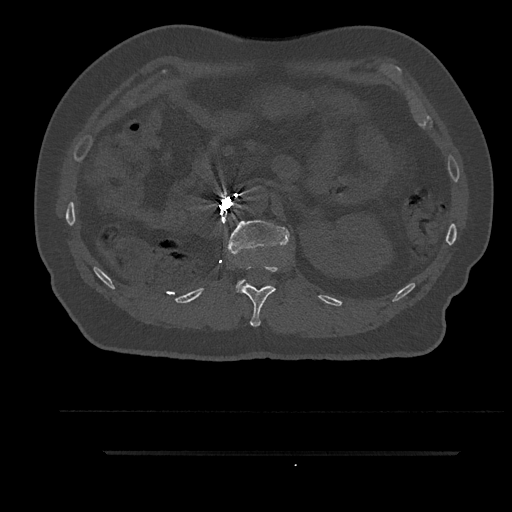
CT including the spine, one axial slice. Position 212 of 797 along the scan axis. Reconstruction kernel Br40s/3. Bone window (W 1800 / L 400 HU). 0.5 mm slice thickness. 512 × 512 image matrix, field of view 432 × 432 mm. Male patient, age 63 years. Case-level facts recorded for this patient, not image findings: primary cancer: renal; vertebrae with lytic lesions (as recorded): T8.
Annotated regions visible in this slice (semi-automatically segmented with operator editing):
- L1 vertebra: box from (x=228, y=220) to (x=289, y=292) px
- T12 vertebra: (x=238, y=265)–(x=278, y=327)